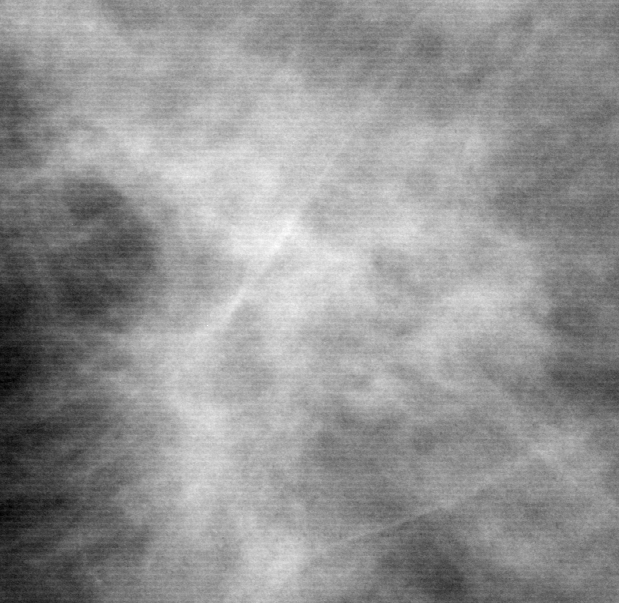
Cropped region of a digitized screen-film mammogram centred on a radiologist-marked abnormality, left breast, CC view.
Finding: mass, shape irregular, margins spiculated; BI-RADS assessment category 5; pathology result (as recorded, not read from the image): malignant.